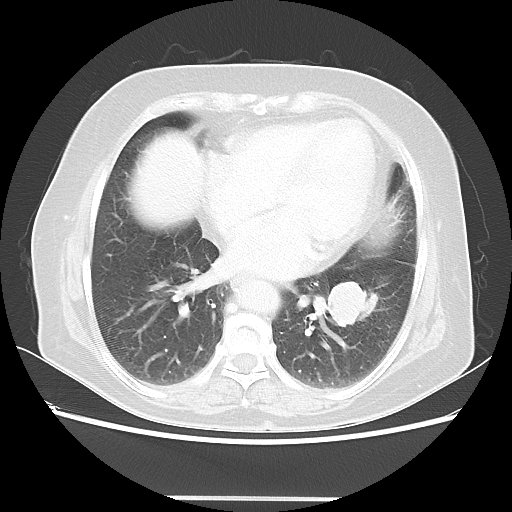
Chest CT, one axial slice; position 23 of 56 along the scan axis; 100 kVp; lung window (W 1500 / L -600 HU); 5 mm slice thickness; 512 × 512 image matrix, field of view 360 × 360 mm. Female patient, age 73 years. Case-level facts recorded for this patient, not image findings: clinical TNM (as recorded): T1c N0 M0.
Annotated regions visible in this slice (bounding box drawn by a radiologist):
- lung tumour (recorded histology: adenocarcinoma): bounding box [x1, y1, x2, y2] px = [321, 277, 387, 333]